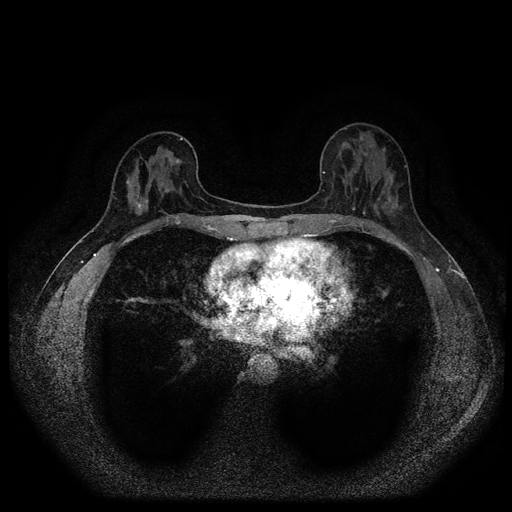
Breast MRI (dynamic contrast-enhanced, multi-phase), one axial slice. Slice 38 of 116 in the series (ordered by position). Dynamic contrast-enhanced series, time point 2 of 5 at this slice position (early post-contrast). 1.5 T. TE 2.7 ms, TR 5.4 ms. 2 mm slice thickness. 512 × 512 image matrix, field of view 330 × 330 mm. Patient: female, 42 years.
Outlined on this slice (semi-automatic segmentation, software-assisted and operator-edited):
- breast lesion (labelled benign in the annotation): bounding box (x1, y1, x2, y2) in pixels: (381, 147, 386, 153)